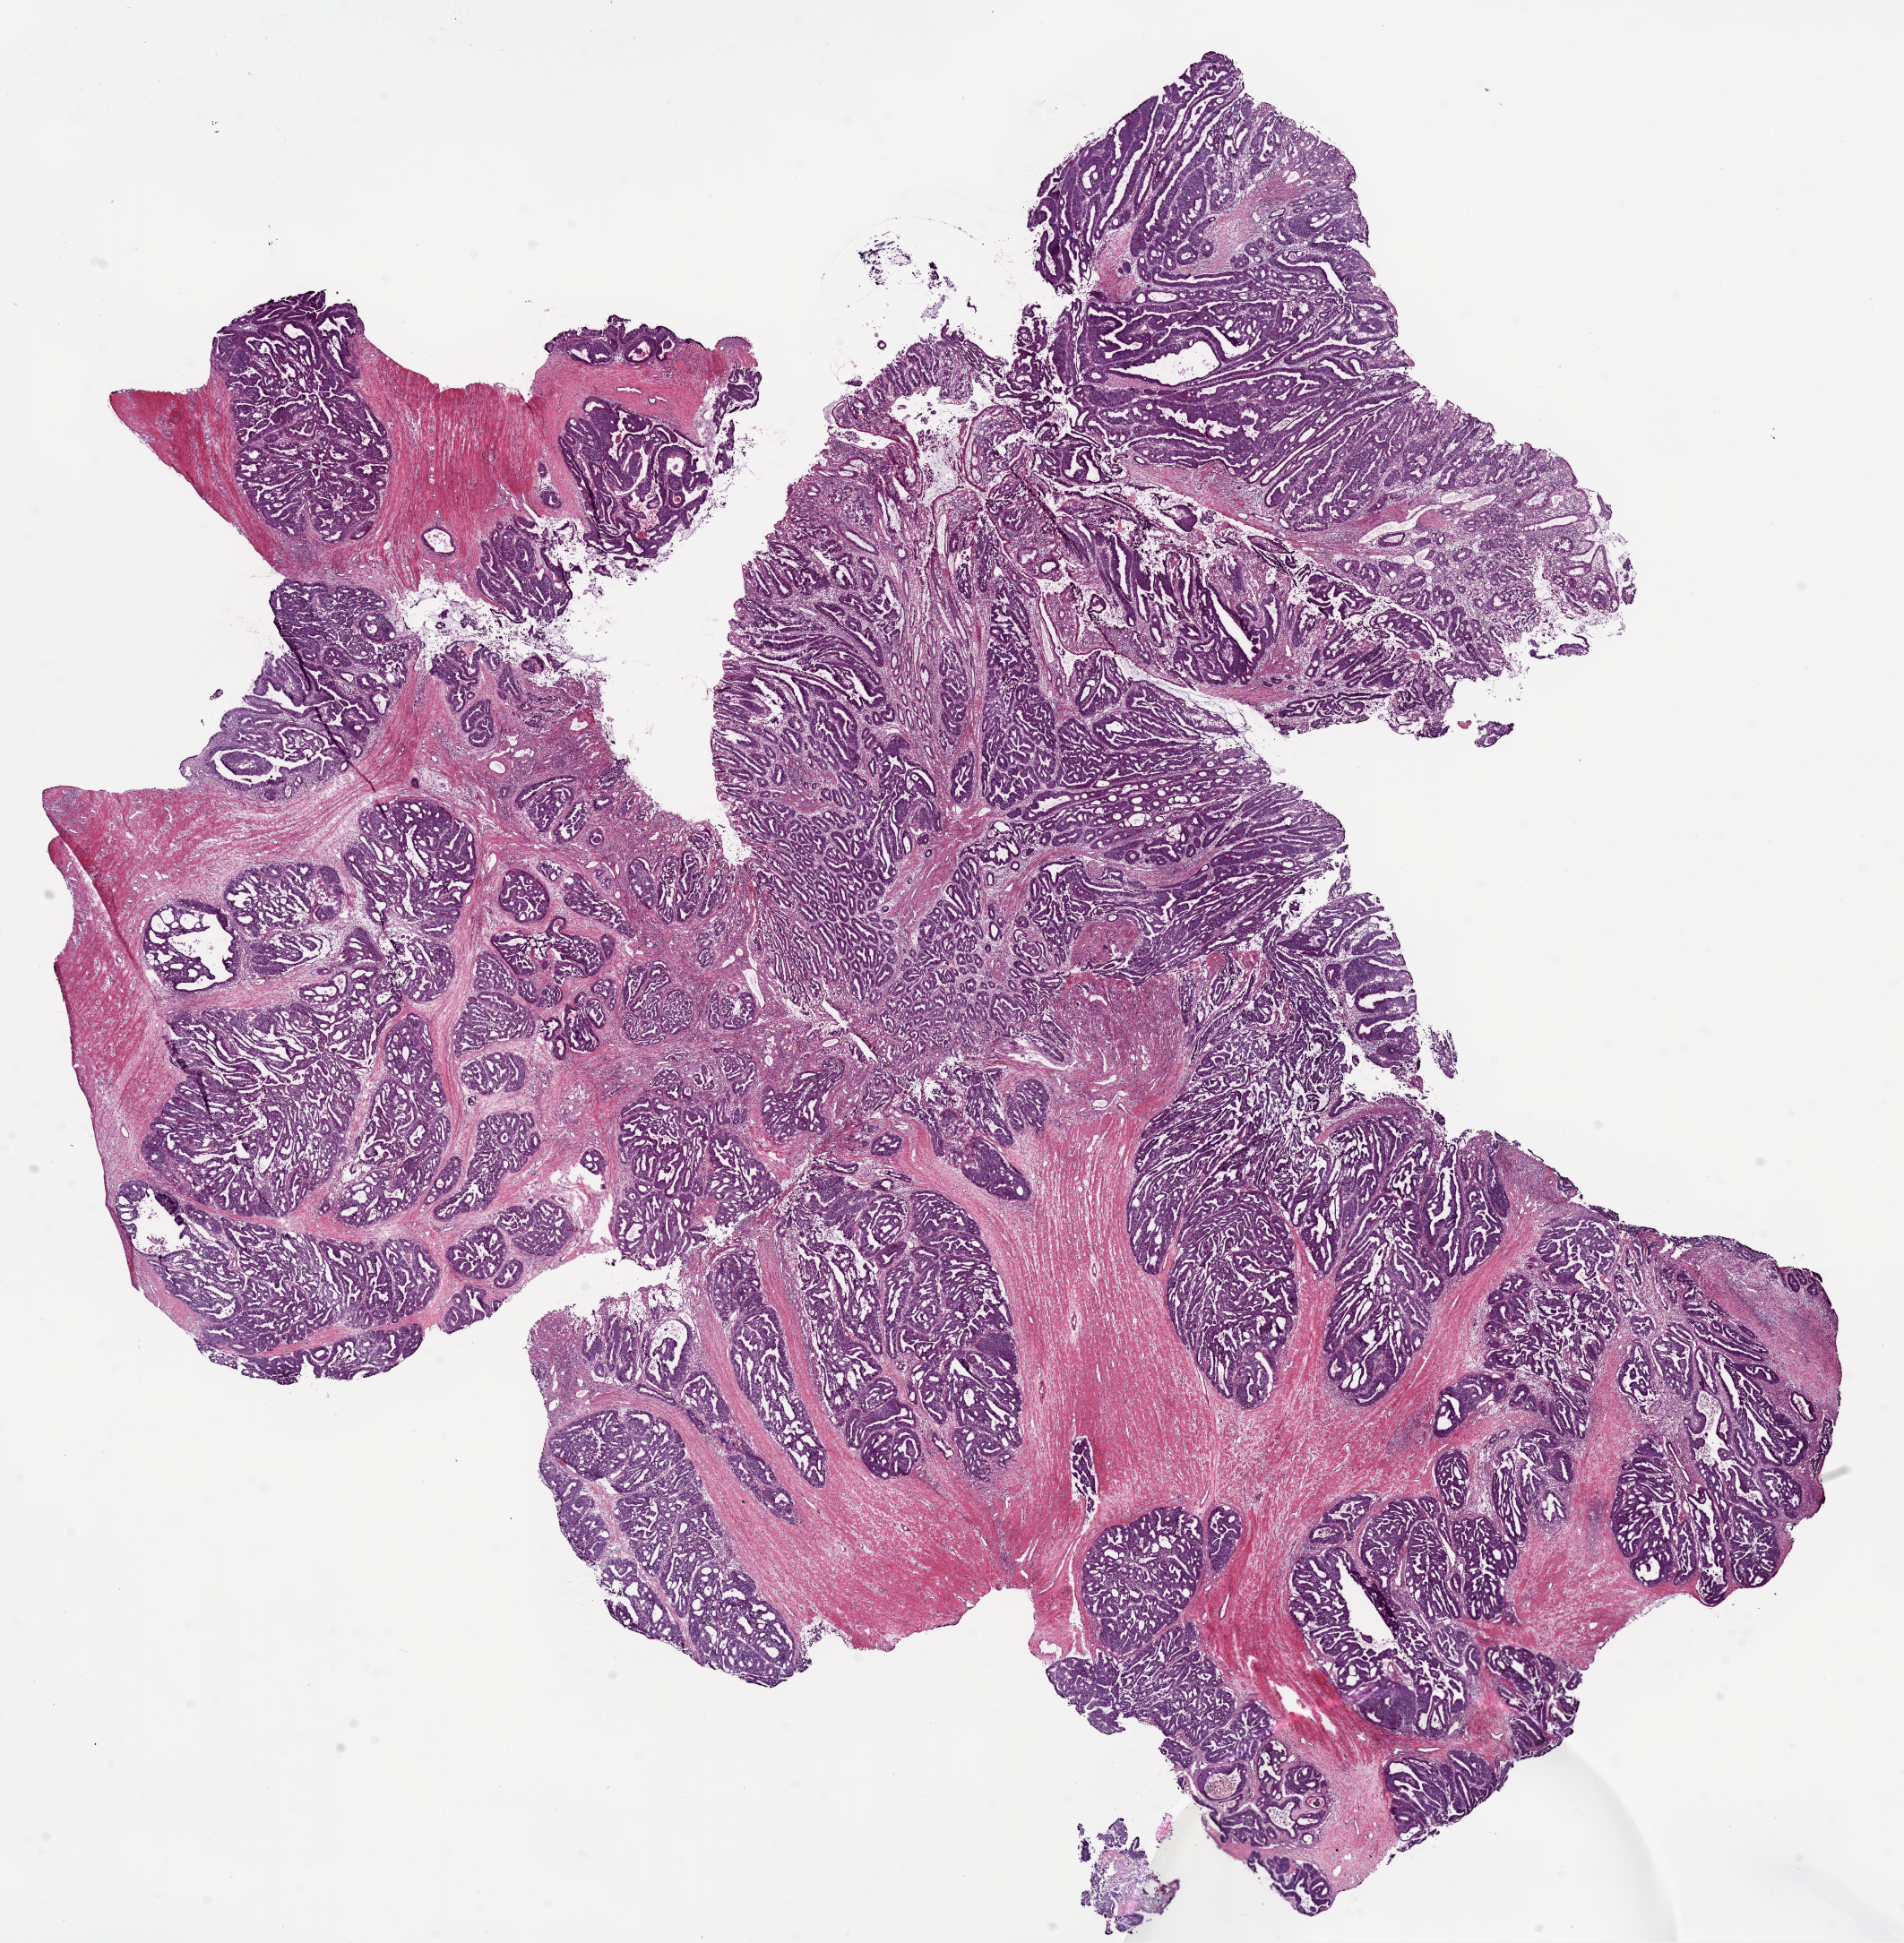
Whole-slide histology image, Hematoxylin and eosin (H&E) stained — a low-resolution overview of the entire scanned area, about 17.1 x 17.4 mm. Frozen section from the bottom of the tissue portion. Primary tumour sample from the rectum. Female patient; age at initial diagnosis 49 years. Slide review estimates, as recorded: tumour cells 74%, tumour nuclei 75%, normal cells 3%, stromal cells 20%, necrosis 3%.
• lymph nodes positive (case pathology): 1 of 22 examined
• AJCC pathologic stage: IIIB
• diagnosis: Adenocarcinoma, NOS (rectosigmoid junction)